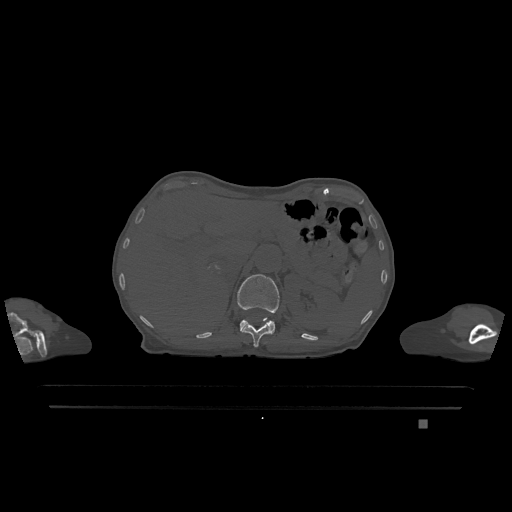
CT including the spine, one axial slice. Slice 503 of 1317 in the series (ordered by position). Bone window (W 1800 / L 400 HU). 0.5 mm slice thickness. 512 × 512 image matrix, field of view 500 × 500 mm. Patient: female, 74 years. From the clinical record (not read from this slice): primary cancer: lung; vertebrae with lytic lesions (as recorded): T1, T4, T5, T6, L4, L5.
Outlined on this slice (semi-automatically segmented with operator editing):
- L1 vertebra: bounding box [x1, y1, x2, y2] px = [237, 274, 280, 334]
- T12 vertebra: [242, 318, 271, 347]